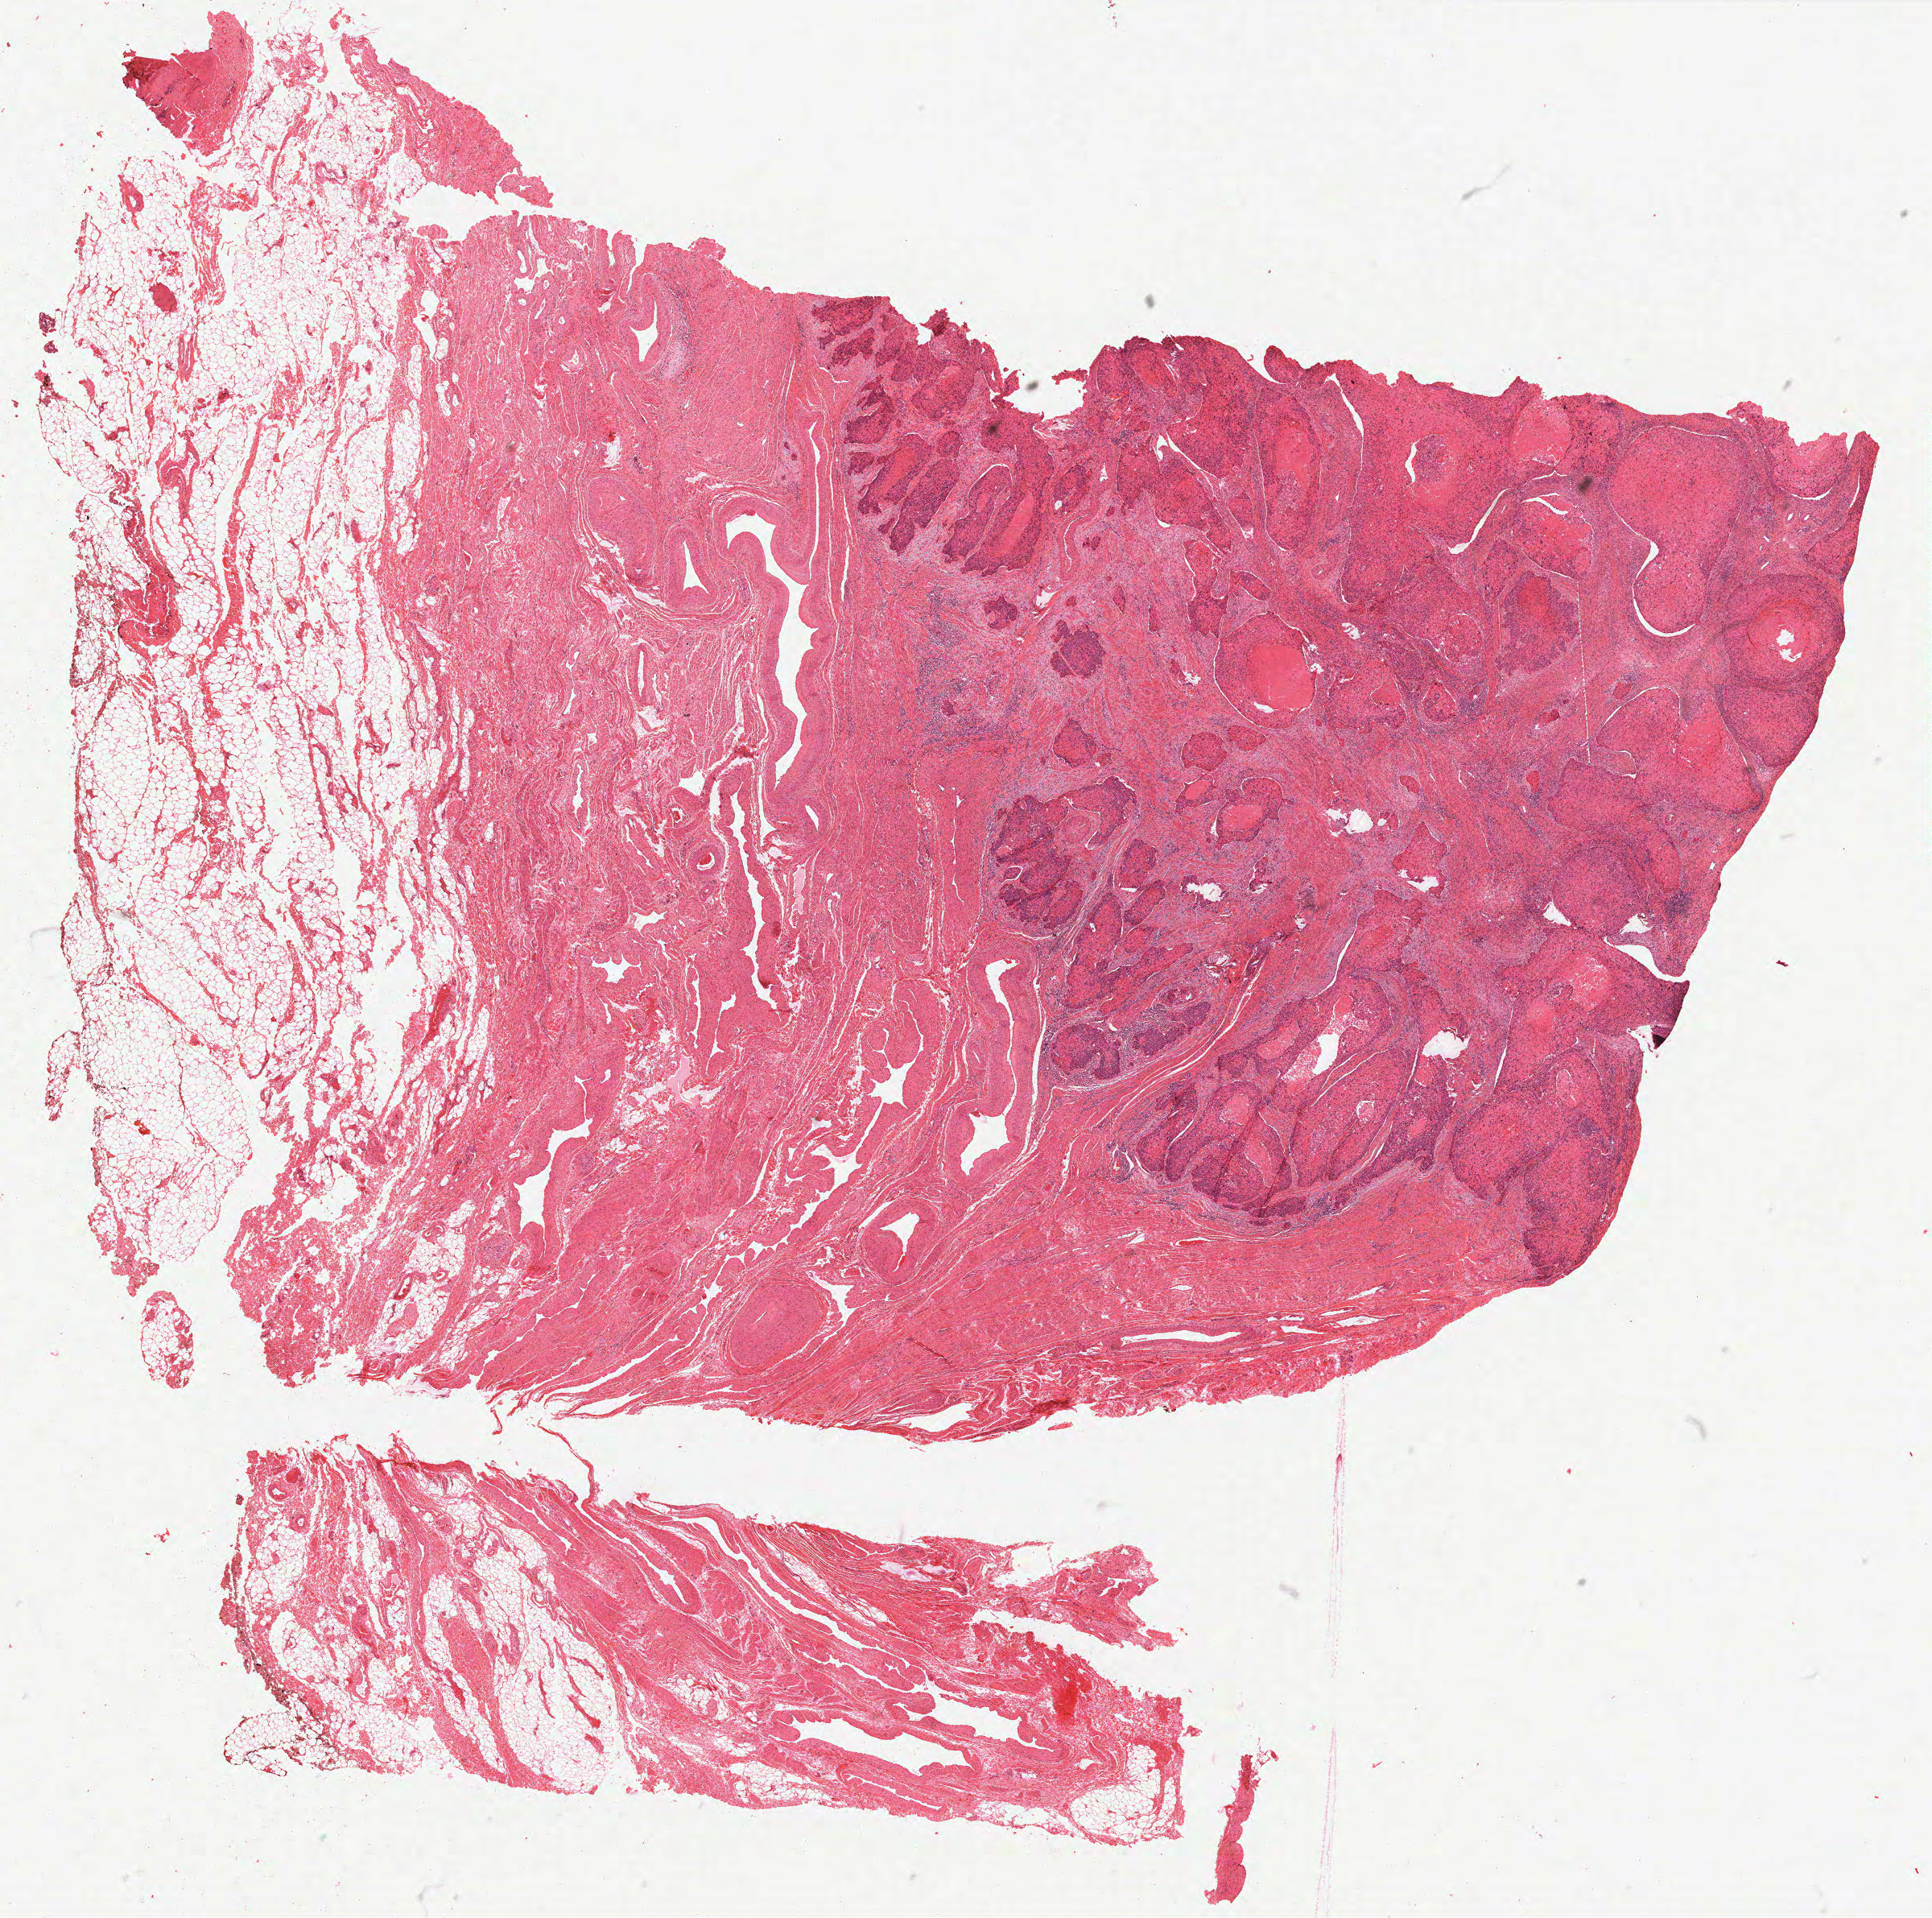
Hematoxylin and eosin (H&E) stained whole-slide image — low-resolution overview of the scanned area, about 19.2 x 19.1 mm (from a 40x scan); formalin-fixed paraffin-embedded (FFPE) diagnostic section; cervix, primary tumour sample. Female, age 44 years at initial diagnosis. Histologic grade: G2 (moderately differentiated).
* diagnosis: Squamous cell carcinoma, keratinizing, NOS (cervix uteri)